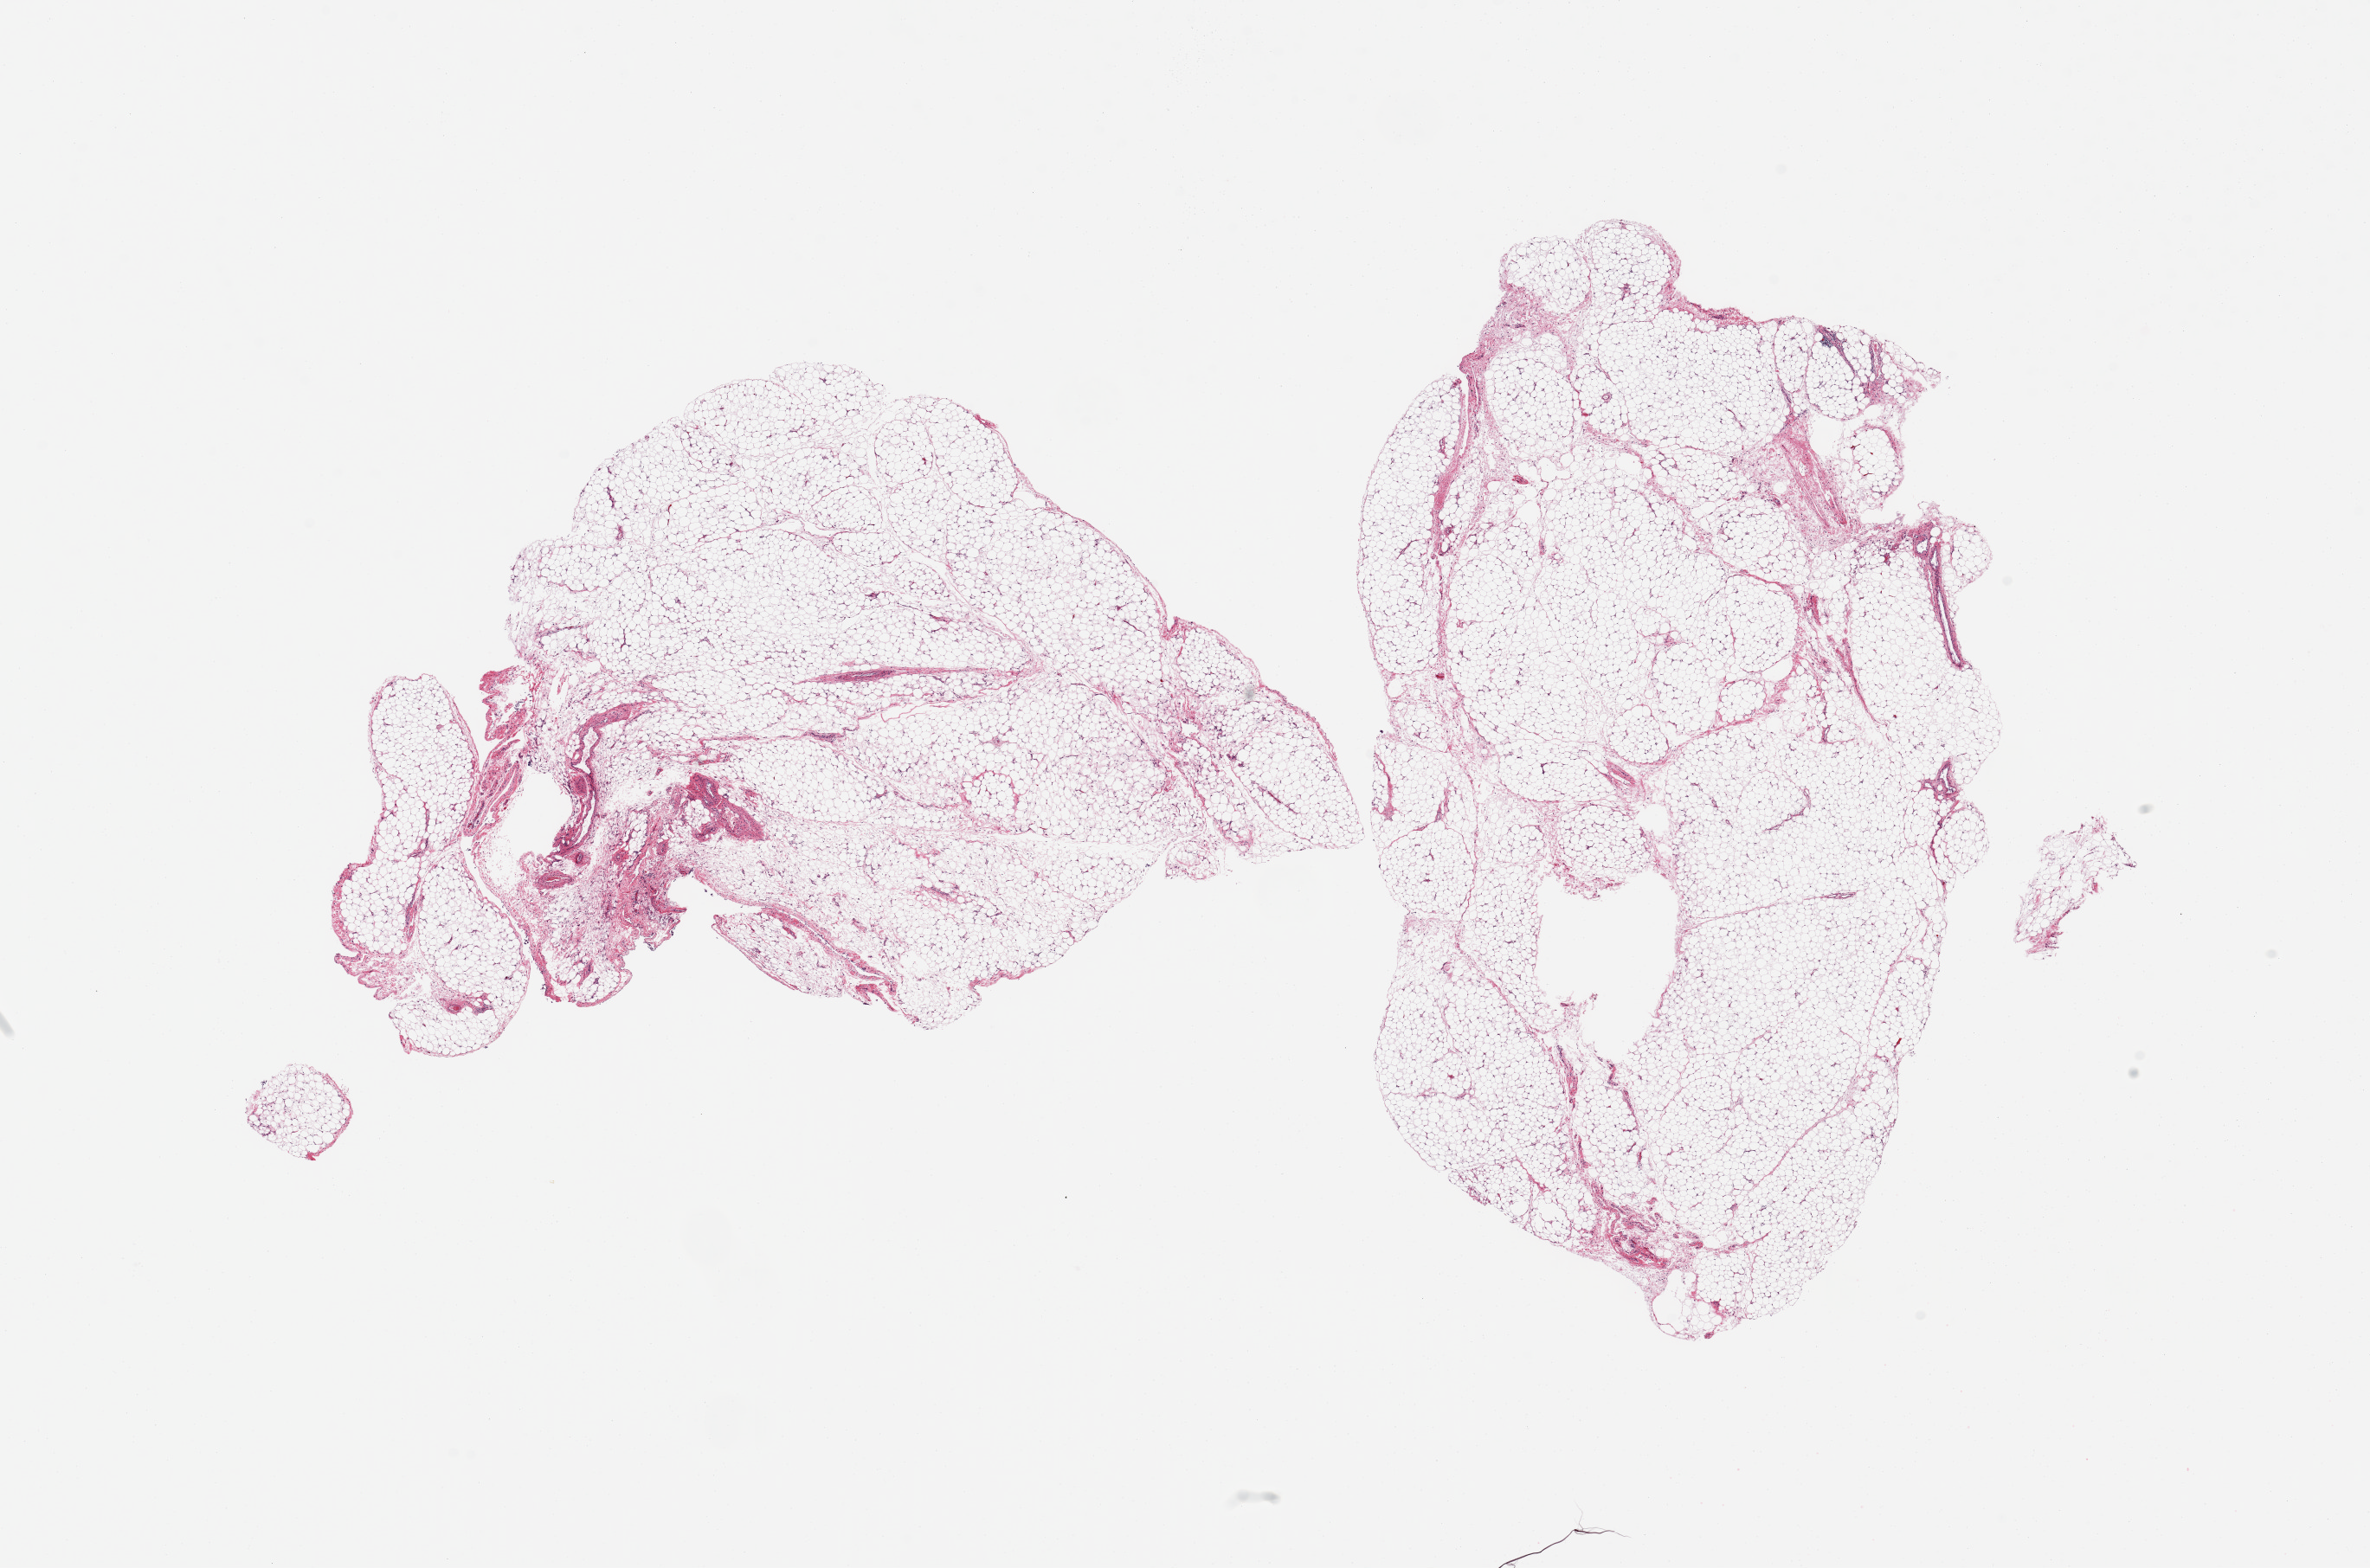
Haematoxylin and eosin whole-slide image — whole scanned area (about 21.7 x 14.3 mm) shown as a low-resolution overview. PAXgene-fixed, paraffin-embedded tissue. Section of omentum (target tissue). Tissue donor sample. Donor: female.
Reviewer comment on this tissue sample: 2 pieces; 5% fibrous content.